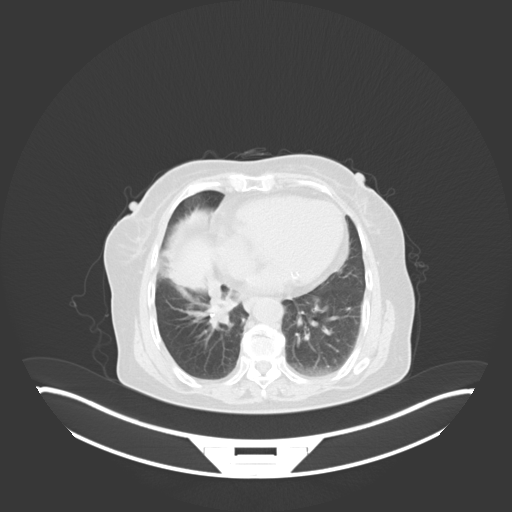
Chest CT, one axial slice. Position 16 of 76 along the scan axis. Reconstruction kernel B30f. 120 kVp. Lung window (W 1500 / L -600 HU). 3 mm slice thickness. 512 × 512 image matrix, field of view 500 × 500 mm. Patient: female, 75 years. From the clinical record (not read from this slice): clinical TNM (as recorded): T1b N0 M1a; histopathological grade: G1.
Annotated regions visible in this slice (rectangle marked by the reading radiologist):
- lung tumour (recorded histology: squamous cell carcinoma): bounding box [x1, y1, x2, y2] px = [205, 296, 238, 329]